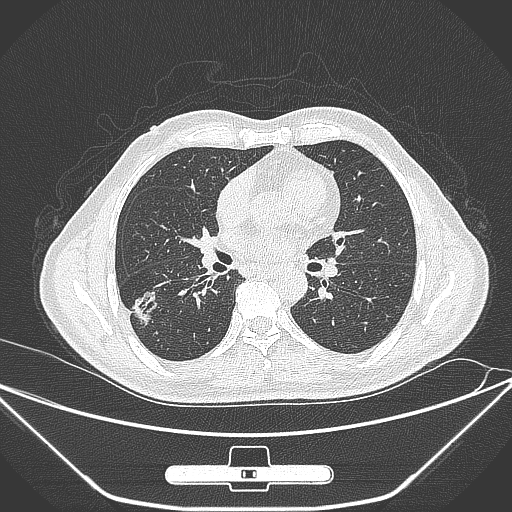
Chest CT, one axial slice; slice 146 of 309 in the series (ordered by position); lung window (W 1500 / L -600 HU); 1 mm slice thickness; 512 × 512 image matrix. Patient: male, 71 years. Case-level facts recorded for this patient, not image findings: clinical TNM (as recorded): T1c N0 M0.
Outlined on this slice (rectangle marked by the reading radiologist):
- lung tumour (recorded histology: adenocarcinoma): bounding box <129,286,160,327> (left, top, right, bottom; pixels)